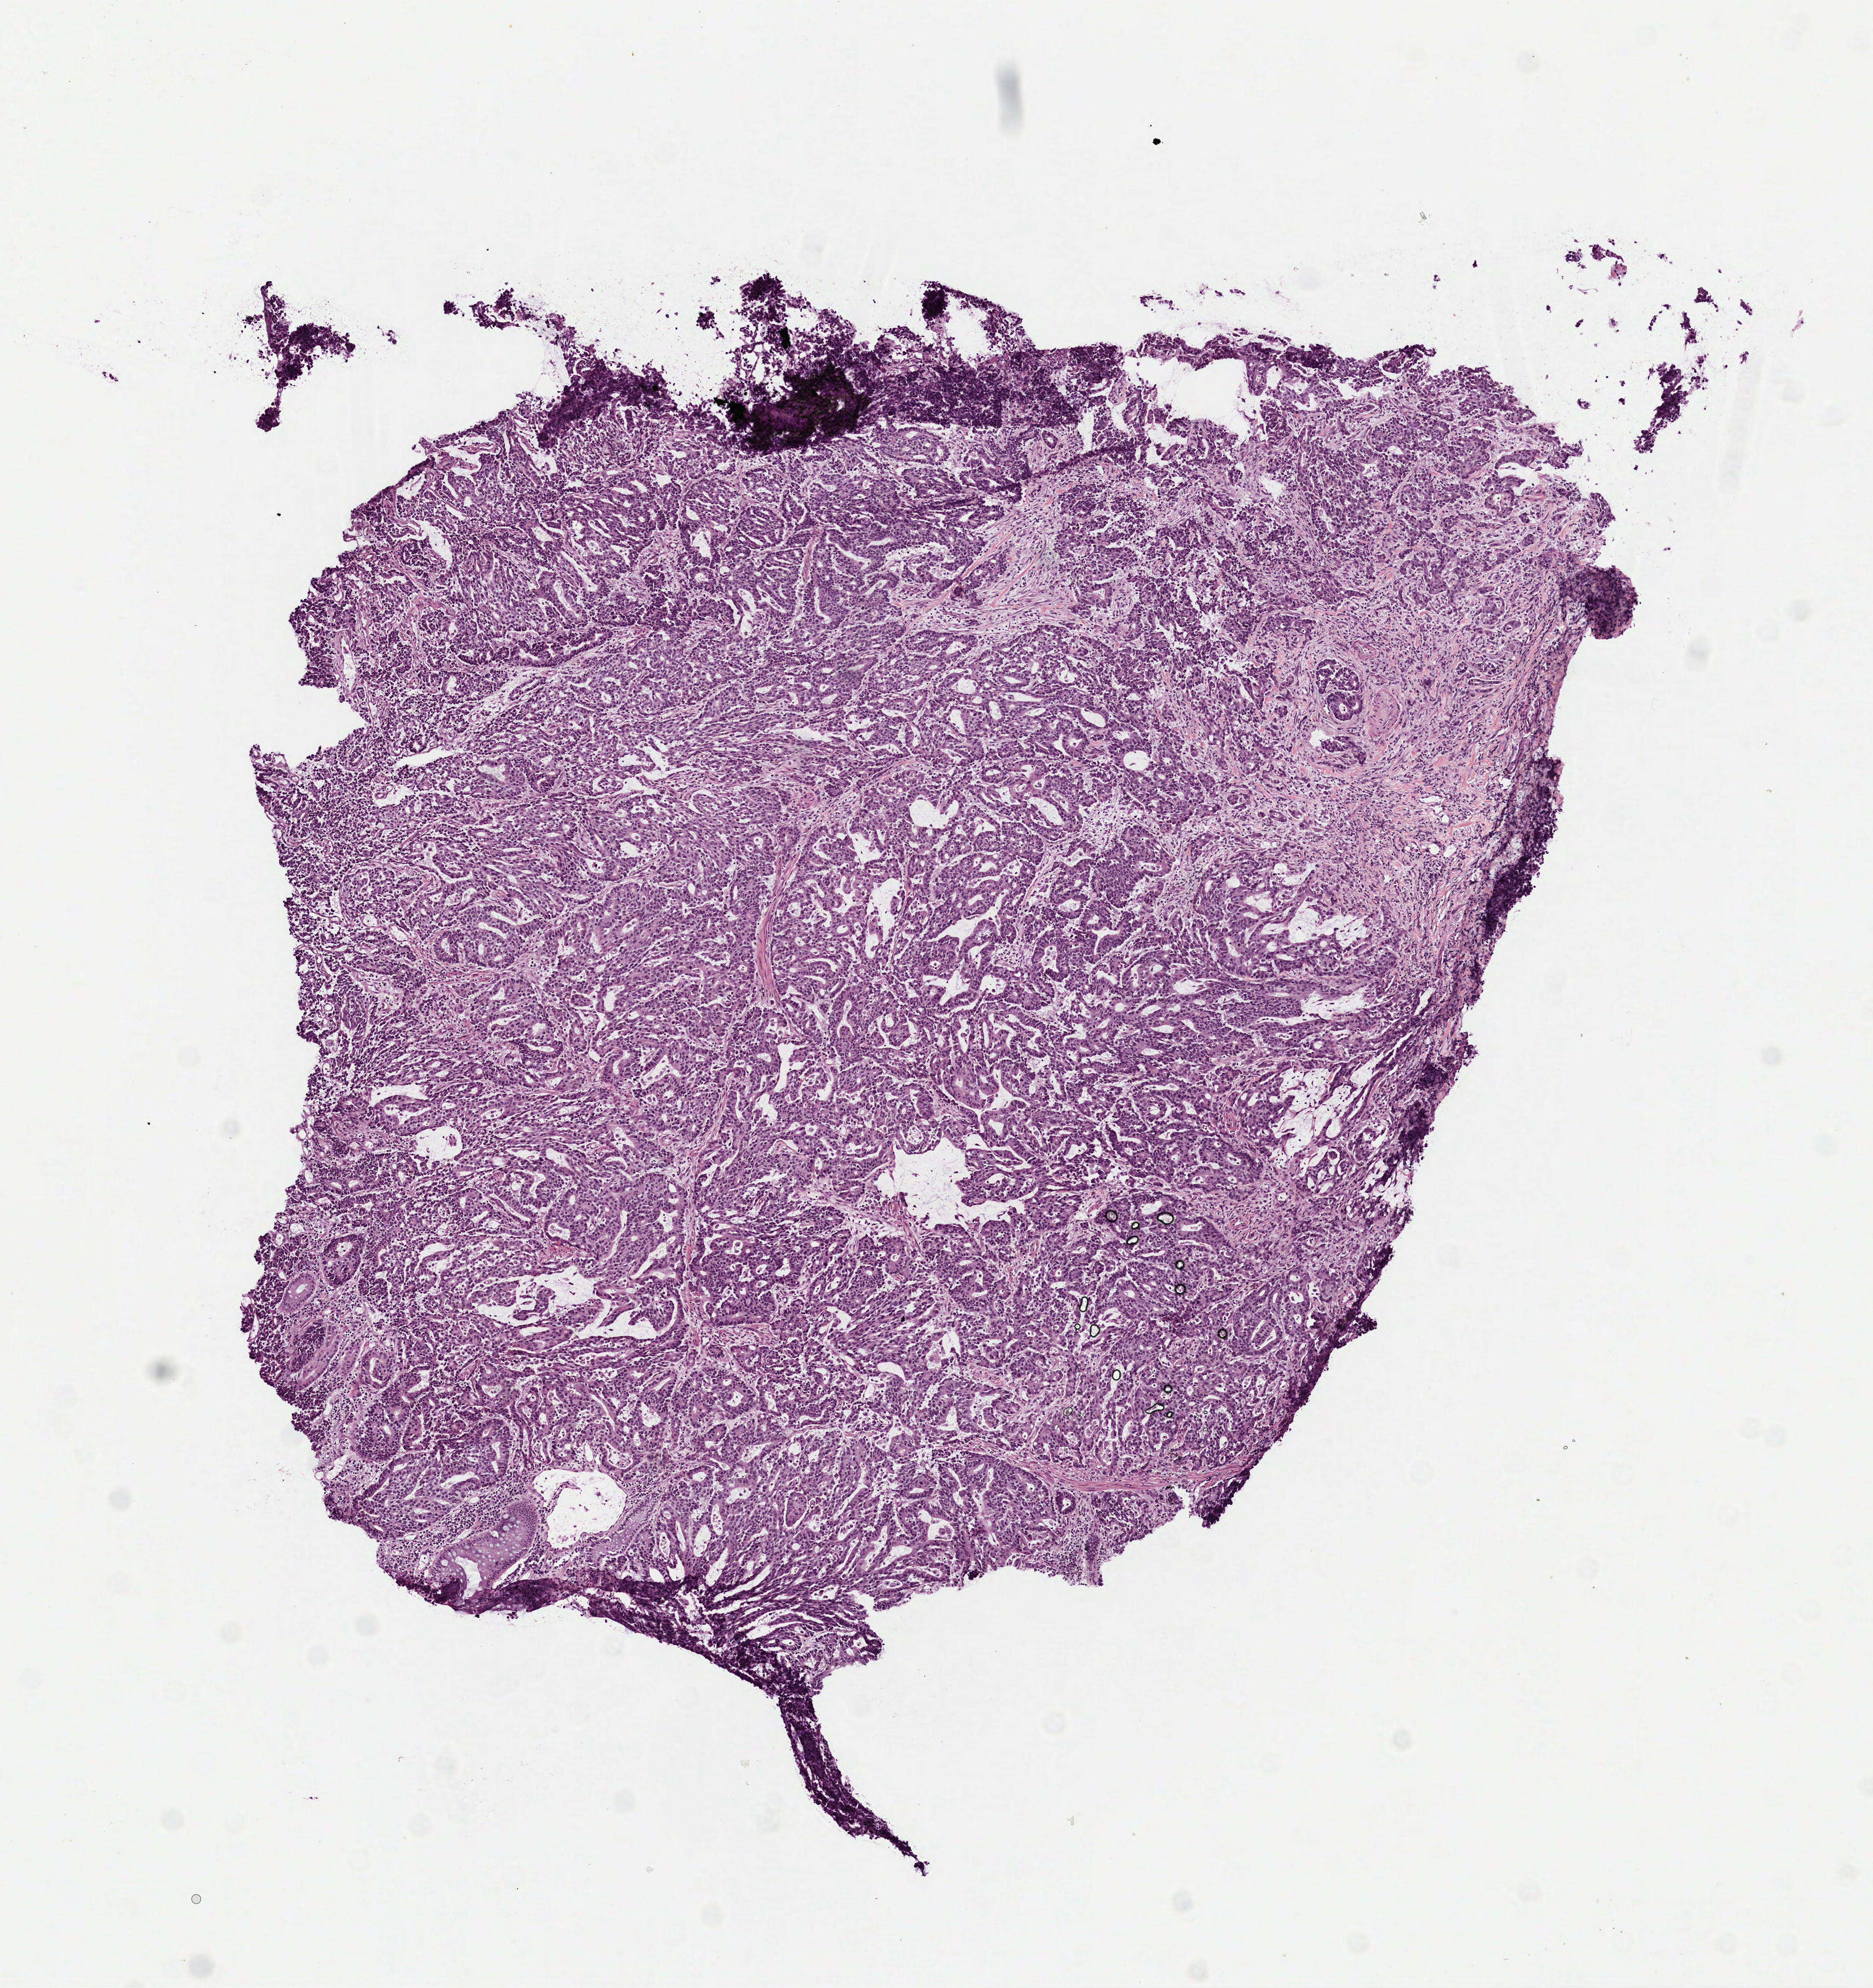
Digitized H&E-stained tissue section (whole slide), shown as a low-resolution overview of the whole scanned area (about 5.8 x 6.2 mm, from a 40x scan), frozen section, rectum, primary tumour sample. Male patient; age at initial diagnosis 74 years. Slide review estimates, as recorded: tumour cells 98%, tumour nuclei 90%, normal cells 1%, stromal cells 0%, necrosis 1%. Infiltration values recorded for this section: lymphocyte infiltration 2%, monocyte infiltration 1%, neutrophil infiltration 1%.
• histologic diagnosis: Adenocarcinoma, NOS
• lymph nodes positive (case pathology): 27 of 72 examined